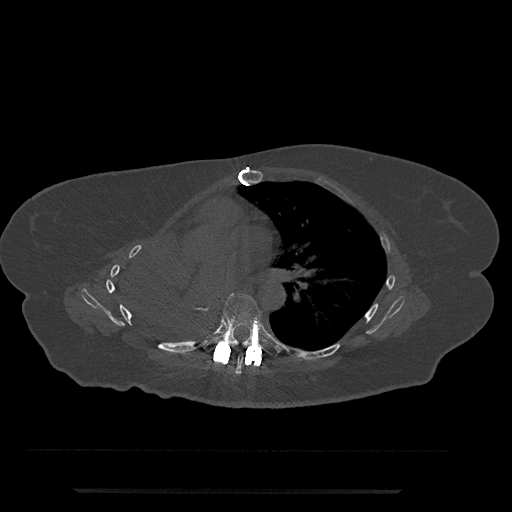
CT including the spine, one axial slice; position 459 of 797 along the scan axis; reconstruction kernel Br40s/3; bone window (W 1800 / L 400 HU); 0.5 mm slice thickness; 512 × 512 image matrix, field of view 440 × 440 mm. Patient: female, 51 years. Case-level facts recorded for this patient, not image findings: primary cancer: neuro; vertebrae with lytic lesions (as recorded): T8.
Outlined on this slice (semi-automatic segmentation, software-assisted and operator-edited):
- T6 vertebra: bounding box [x1, y1, x2, y2] px = [236, 354, 243, 374]
- T7 vertebra: [203, 293, 279, 357]